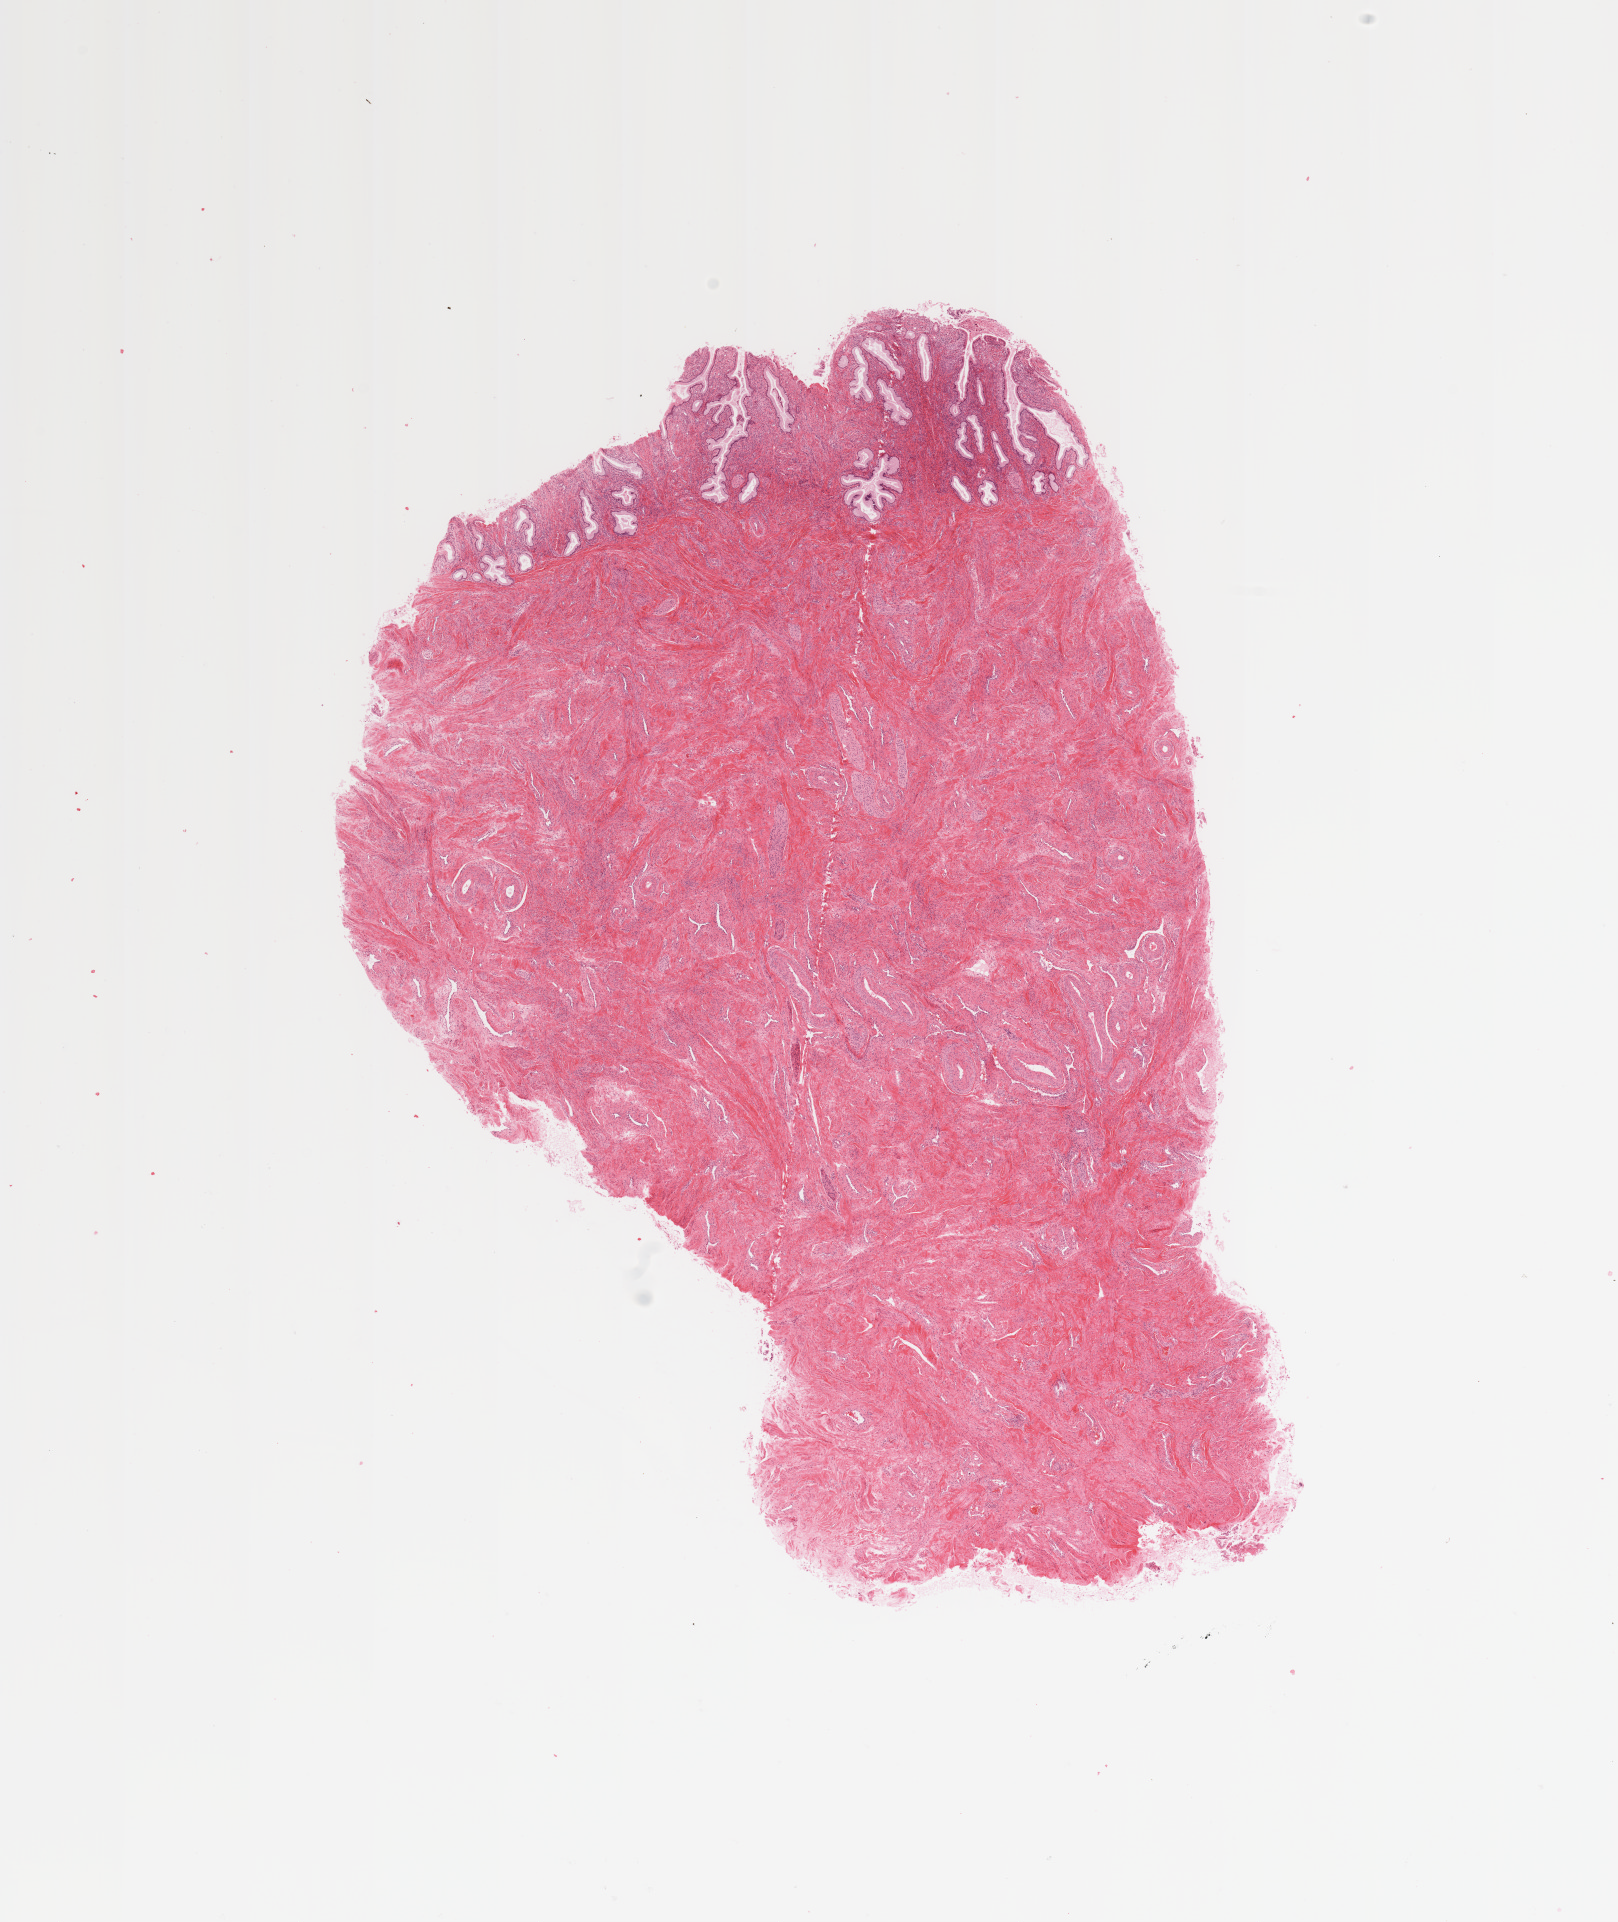
Hematoxylin and eosin (H&E) stained whole-slide image — shown as a low-resolution overview of the whole scanned area (about 12.8 x 15.2 mm, from a 20x scan); normal (non-tumour) tissue sample, uterus. Female, 60 y/o.
This section: normal (non-tumour) tissue from the same patient. Patient diagnosis: Endometrioid adenocarcinoma, NOS.